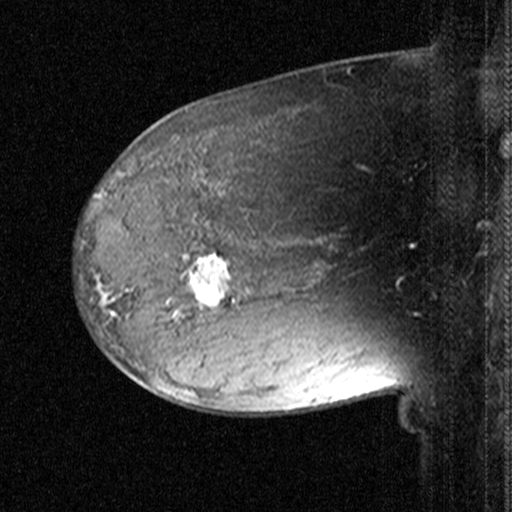
Breast MRI (dynamic contrast-enhanced), one sagittal slice; position 29 of 44 along the scan axis; dynamic contrast-enhanced study with each time point stored as its own series, time point 2 of 3 at this slice position (early post-contrast, ordered by acquisition time); 1.5 T; TE 4.5 ms, TR 11 ms; 3 mm slice thickness; 512 × 512 image matrix, field of view 200 × 200 mm. Patient: female, 38 years. Case-level facts recorded for this patient, not image findings: setting: breast cancer imaged before/during neoadjuvant chemotherapy; receptor status: HR-positive, HER2-negative.
Structures marked on this image (semi-automatic segmentation, software-assisted and operator-edited):
- analysis volume of interest (the breast-tissue region the enhancement analysis was run in; not a lesion): box from (x=170, y=232) to (x=259, y=331) px
- tumour enhancement mask (voxels above the 90 % enhancement threshold inside the analysis volume of interest): (x=177, y=253)–(x=235, y=317)